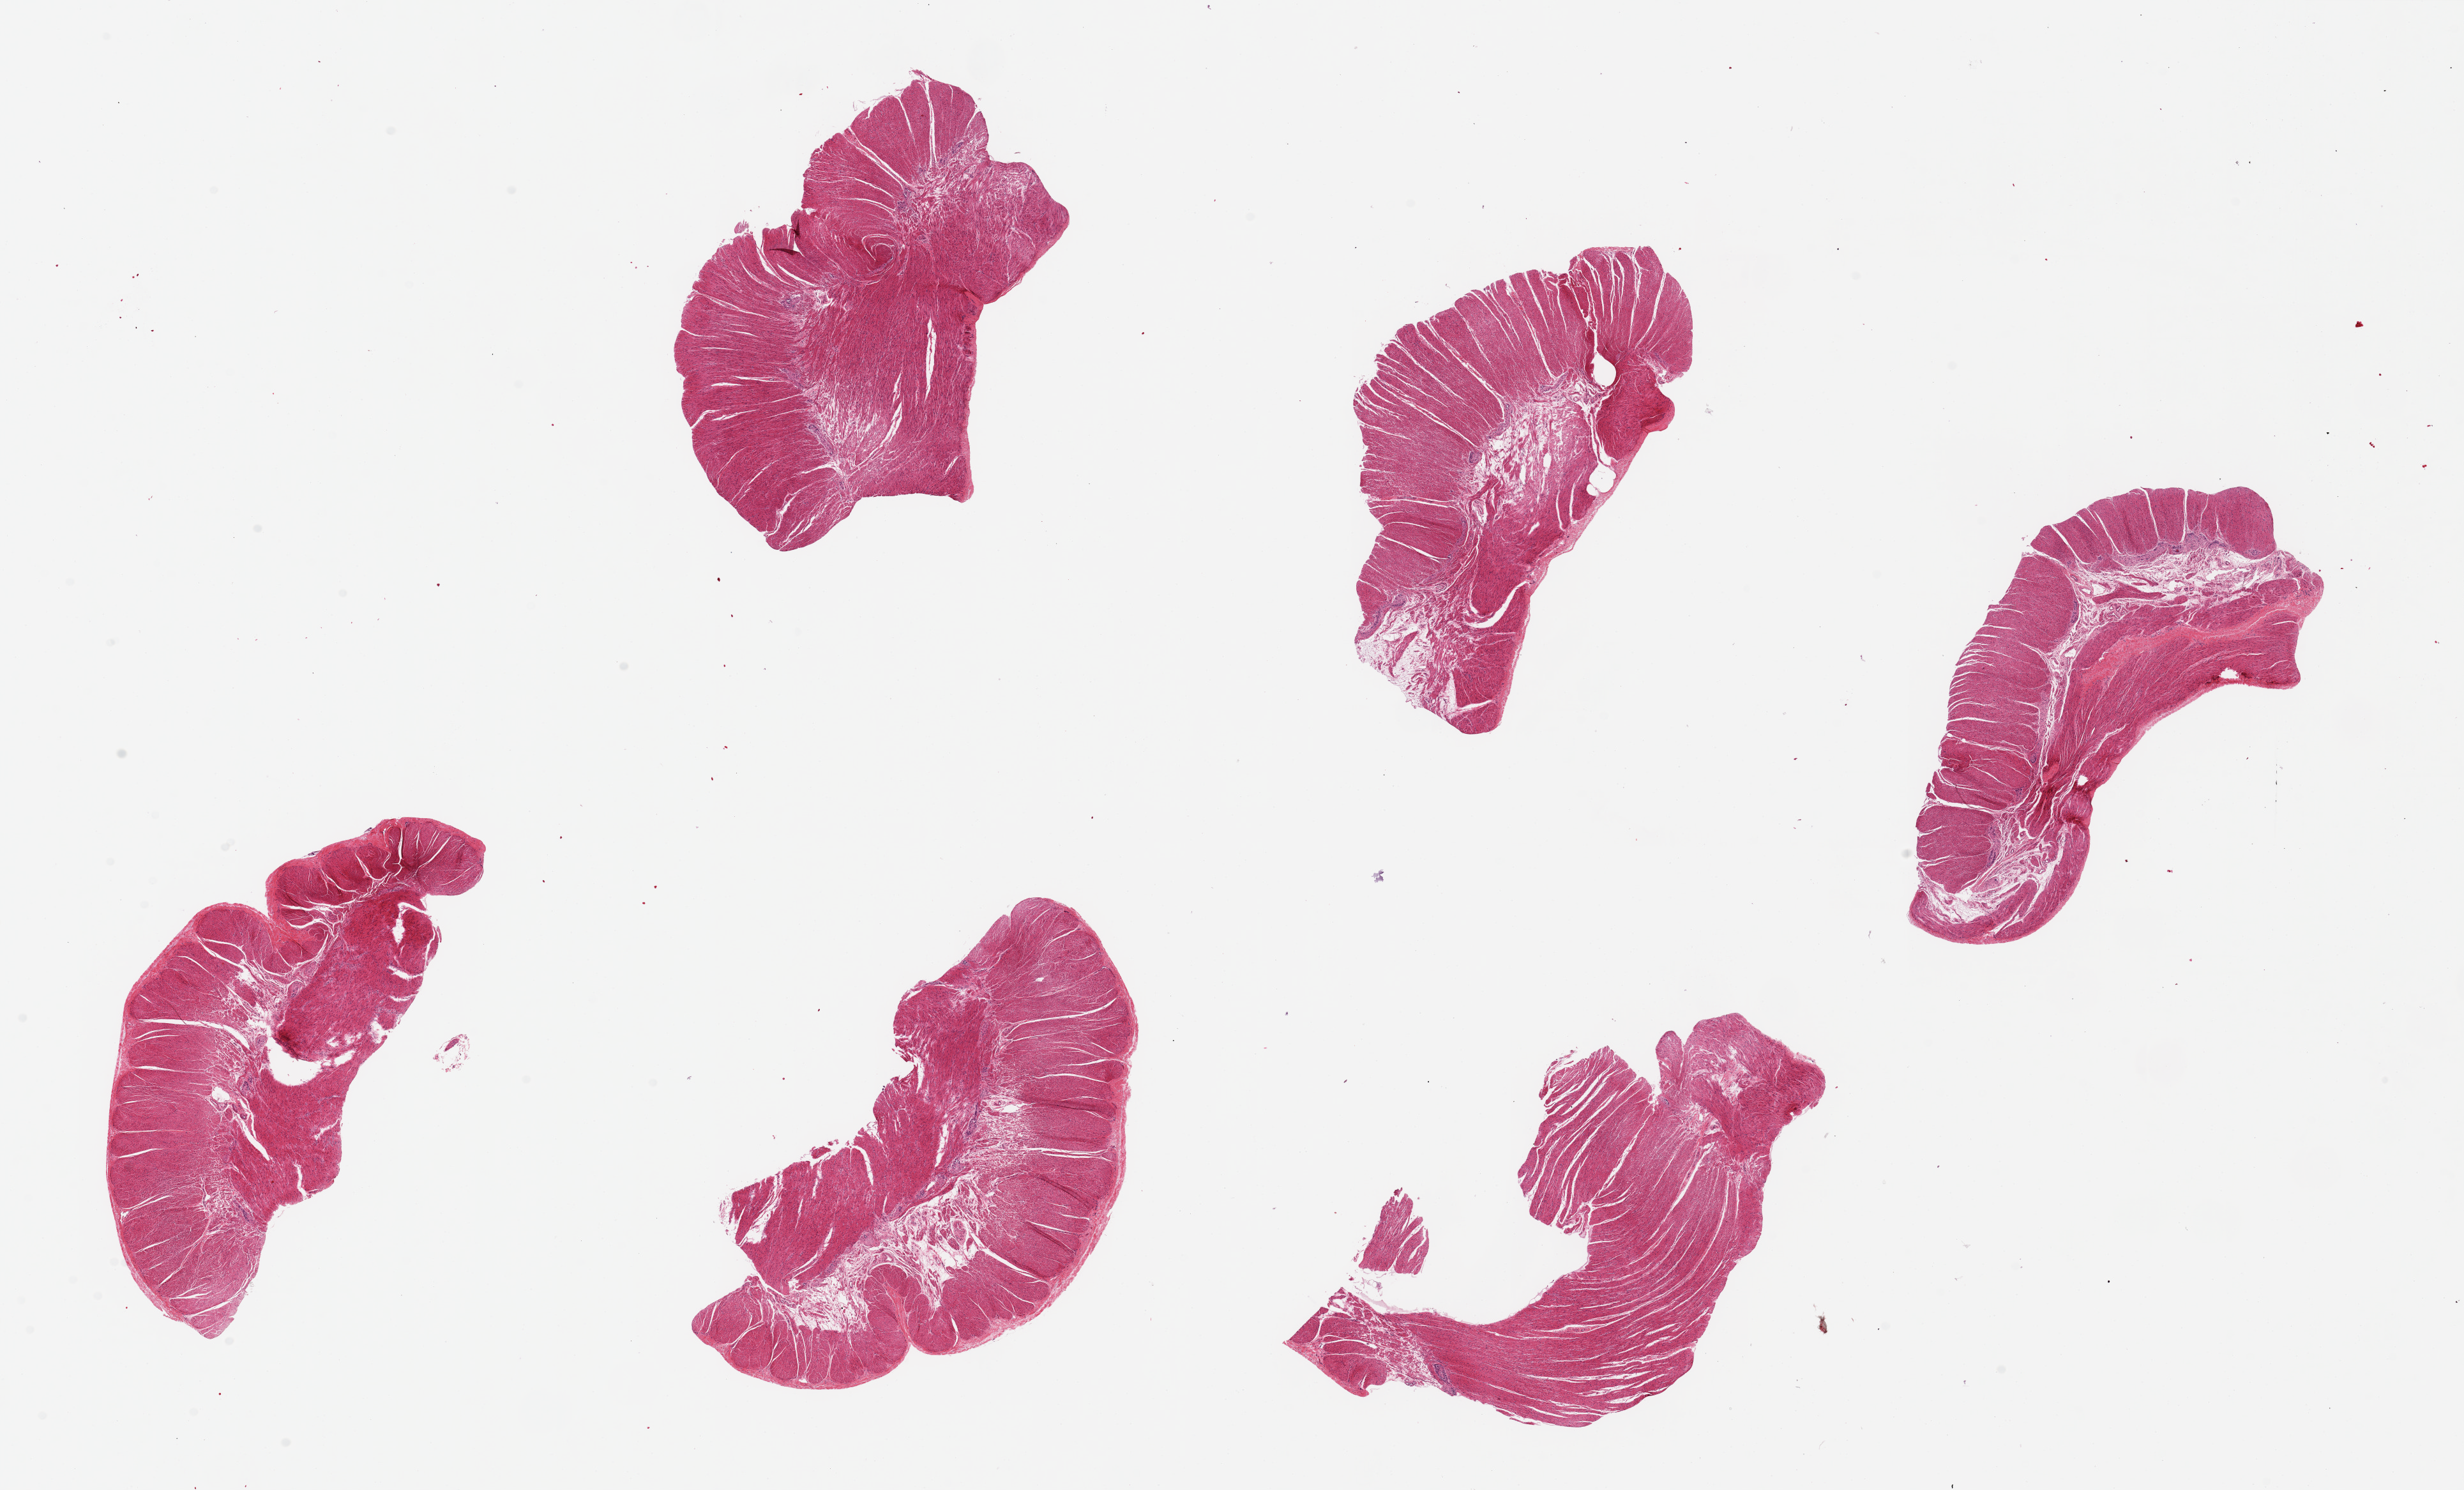
Digitized H&E-stained section — whole scanned area (about 30.5 x 18.4 mm) shown as a low-resolution overview; PAXgene-fixed paraffin-embedded (PFPE) section; section of sigmoid colon (target tissue); tissue donor sample.
Pathologist's review note for this sample: 6 pieces ~6x4mm, all muscularis, good specimens.